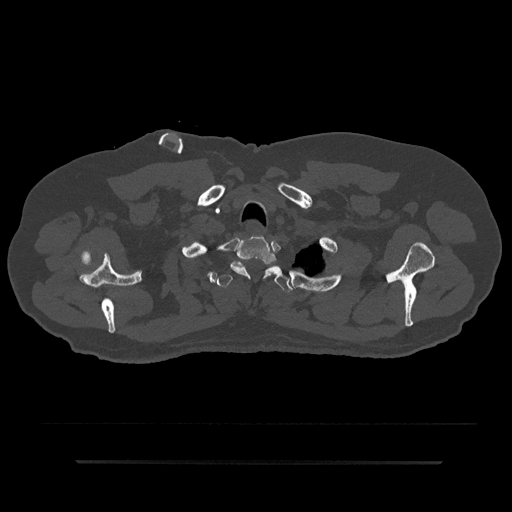
CT including the spine, one axial slice. Slice 722 of 797 in the series (ordered by position). Reconstruction kernel Br40s/3. 120 kVp. Bone window (W 1800 / L 400 HU). 0.5 mm slice thickness. 512 × 512 image matrix, field of view 464 × 464 mm. Patient: male, 59 years. Case-level facts recorded for this patient, not image findings: primary cancer: bile ducts.
Outlined on this slice (semi-automatically segmented with operator editing):
- T1 vertebra: bounding box <230,236,276,278> (left, top, right, bottom; pixels)
- T2 vertebra: <215,265,292,293>